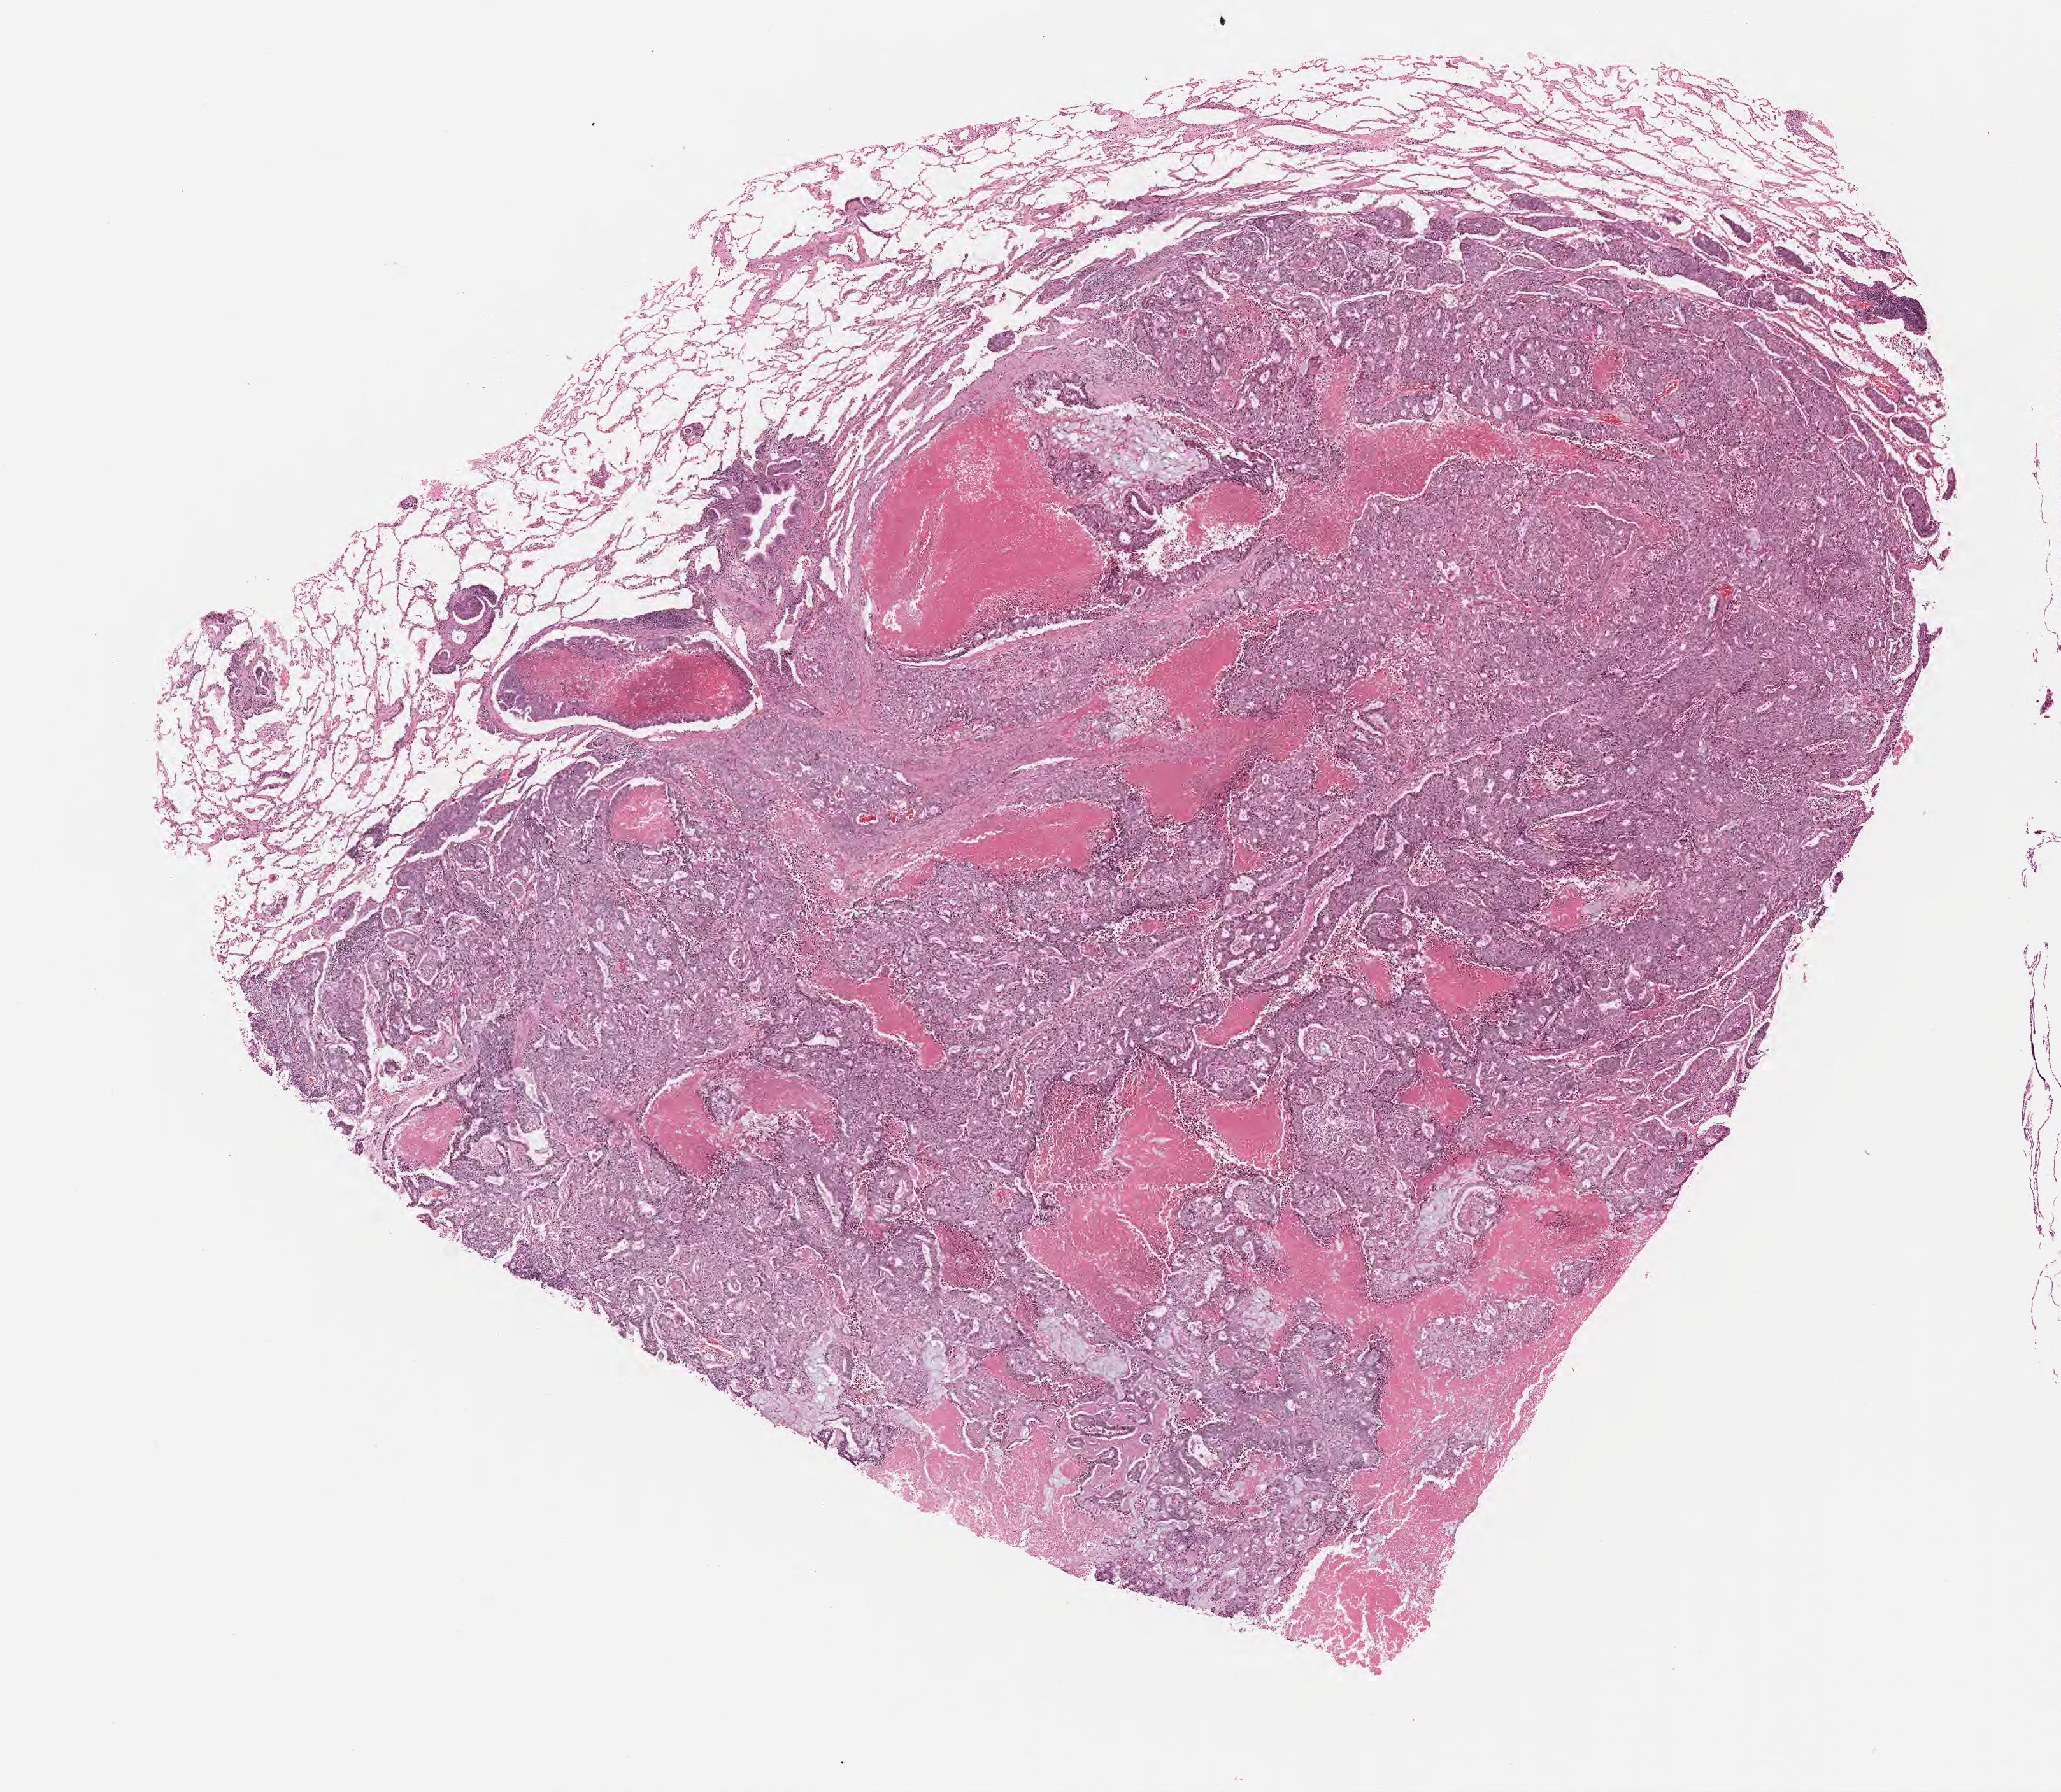
Digitized hematoxylin and eosin (H&E)-stained section, a low-resolution overview of the entire scanned area, about 13.1 x 11.4 mm, FFPE section, specimen: primary tumor, anatomic site: upper lobe of left lung. Patient female; 70 years old. Composition of this section per pathologist review: tumor cells 70%, tumor nuclei 70%, stromal cells 20%, necrosis 7%, normal cells 3%. Infiltration values recorded for this section: lymphocyte infiltration 3%, monocyte infiltration 3%, neutrophil infiltration 5%.
- histologic diagnosis: Adenocarcinoma, NOS
- AJCC pathologic stage: Stage IV